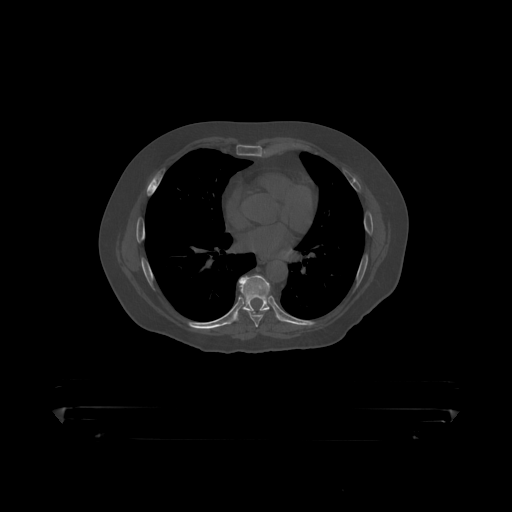
CT including the spine, one axial slice; slice 268 of 390 in the series (ordered by position); reconstruction kernel STANDARD; 120 kVp; bone window (W 1800 / L 400 HU); 512 × 512 image matrix, field of view 650 × 650 mm. Patient: male, 60 years. Case-level facts recorded for this patient, not image findings: primary cancer: prostate.
Annotated regions visible in this slice (semi-automatically segmented with operator editing):
- T7 vertebra: bounding box [x1, y1, x2, y2] px = [245, 310, 267, 319]
- T8 vertebra: [234, 275, 277, 317]